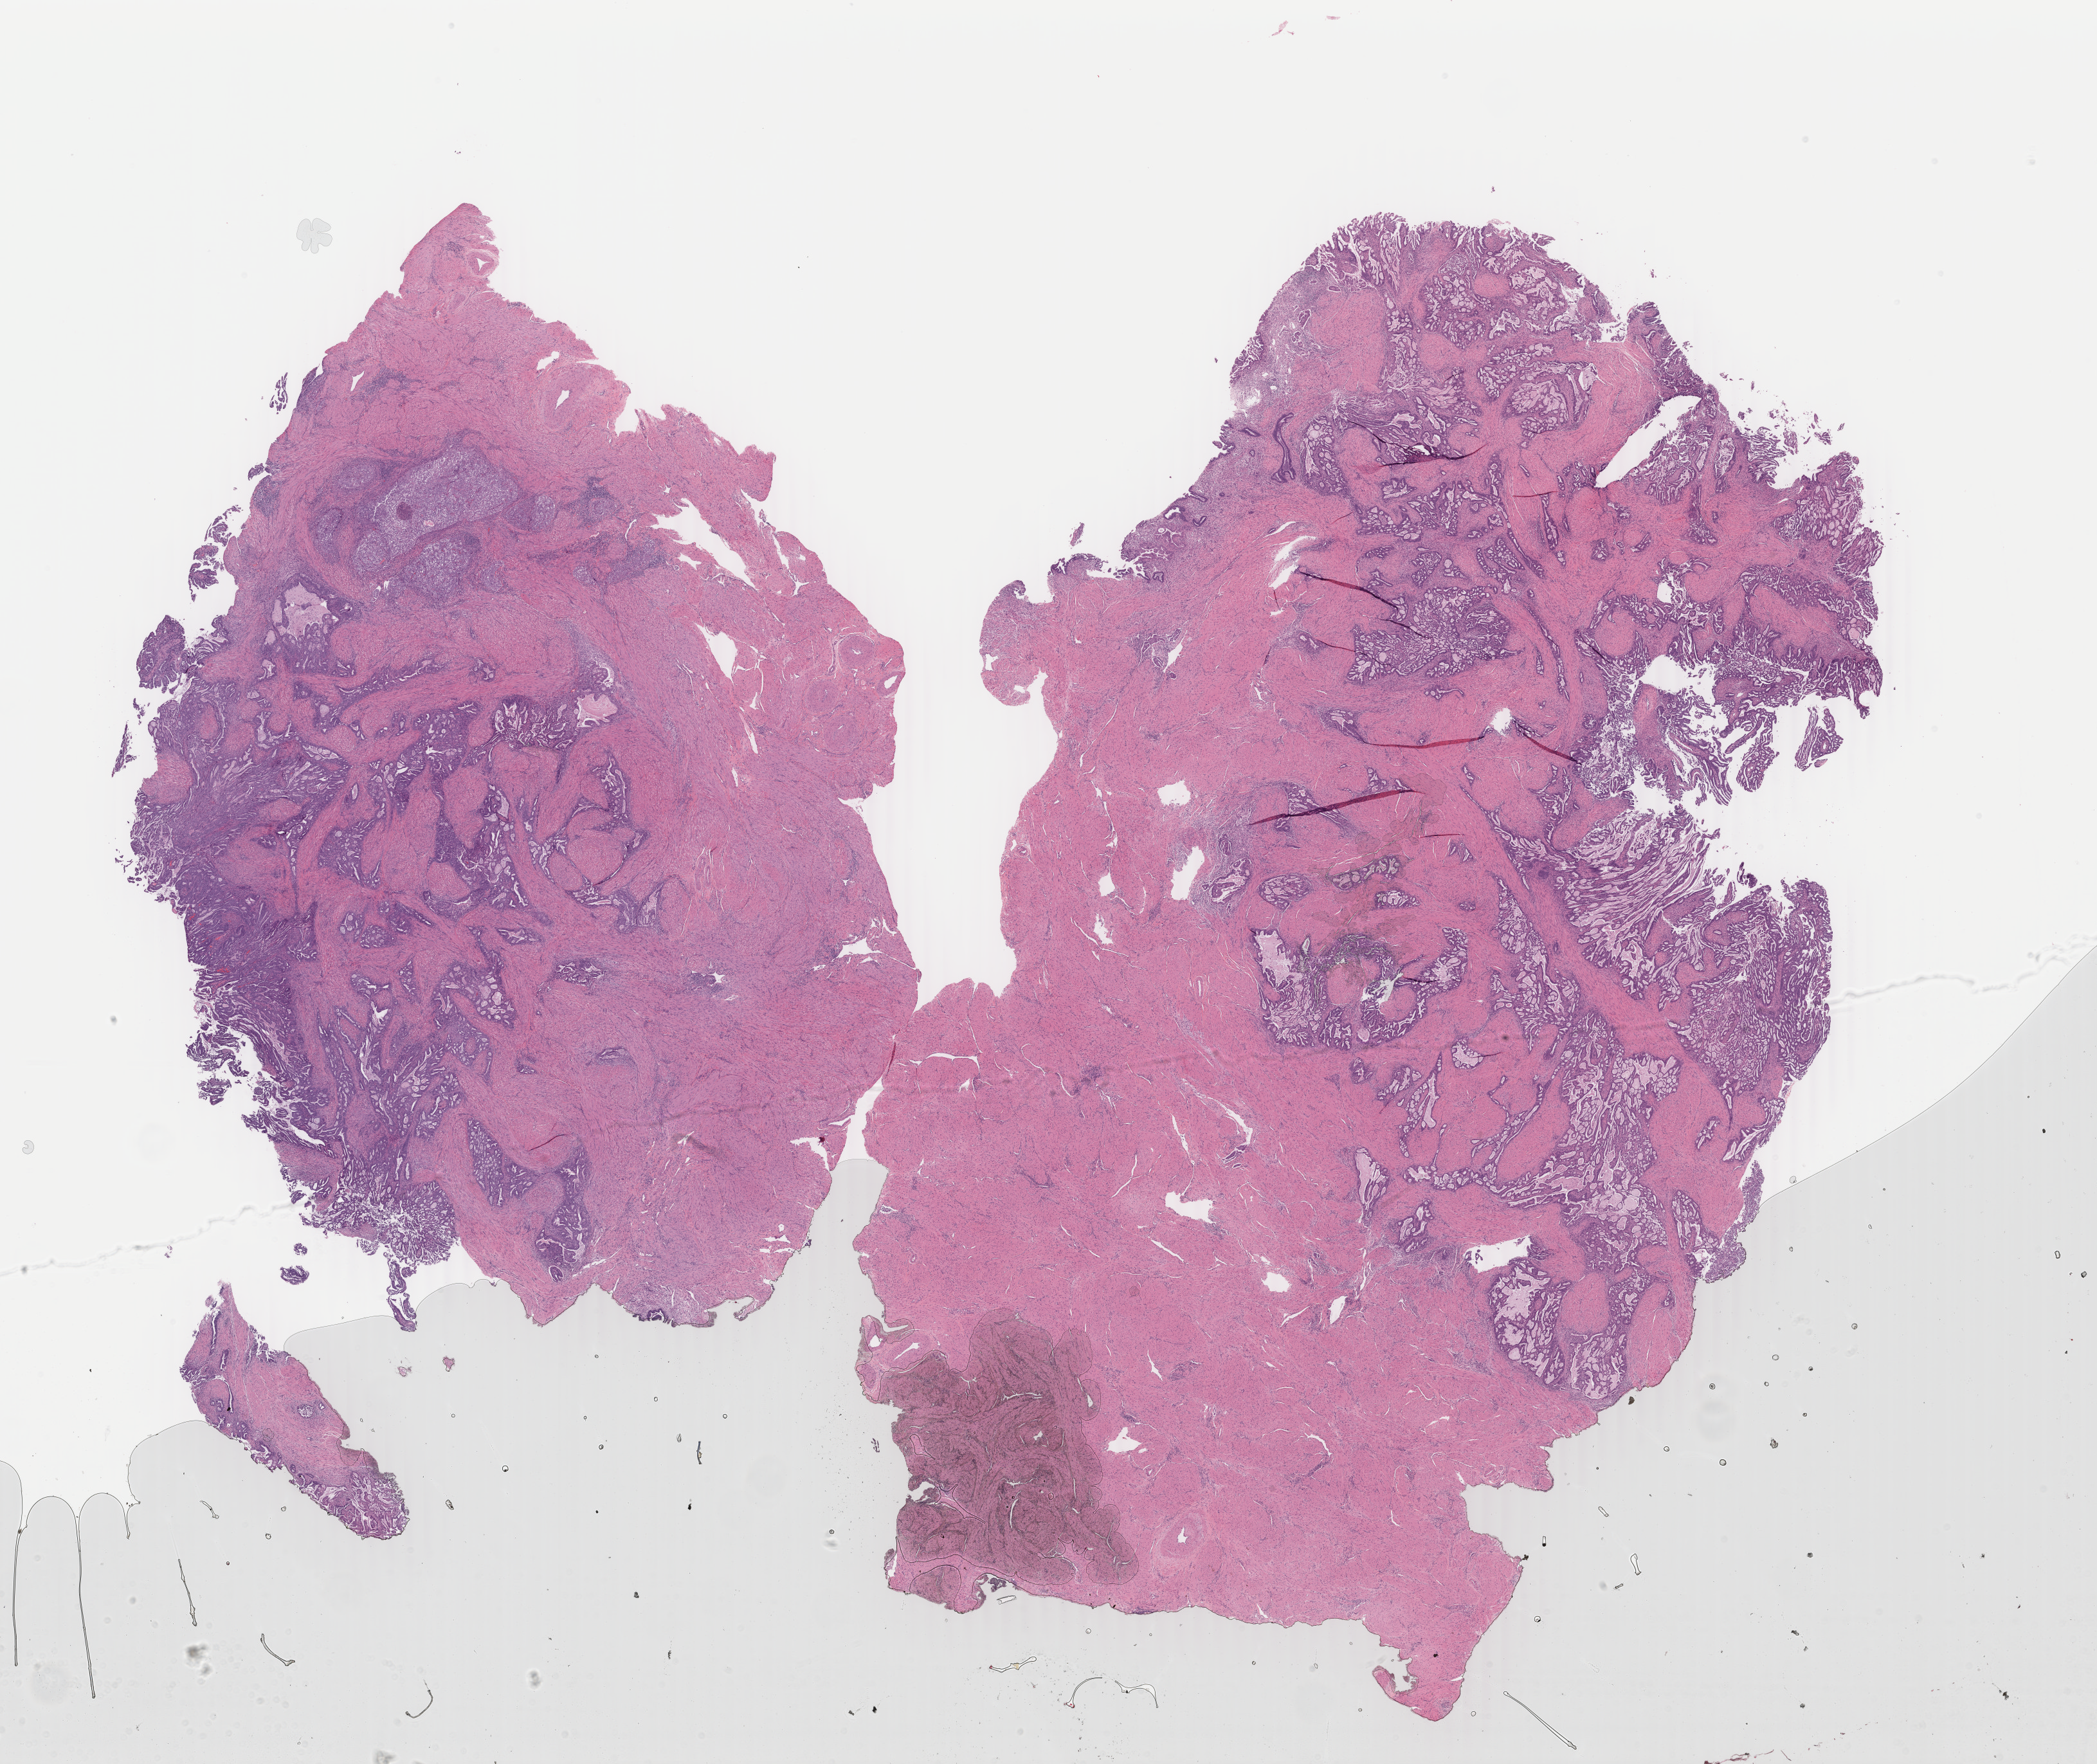
Whole-slide histology image, Hematoxylin and eosin (H&E) stained, whole scanned area (about 25.9 x 21.8 mm, acquisition: 40x scan) shown as a low-resolution overview. Formalin-fixed paraffin-embedded (FFPE) diagnostic section. Uterus, primary tumour sample. Female, age 59 years at initial diagnosis. Histologic grade: G3 (poorly differentiated).
- diagnosis: Endometrioid adenocarcinoma, NOS
- FIGO stage: IIA